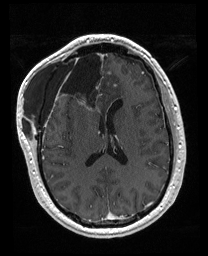
Brain MRI from a brain-tumour surgery series, one axial slice; slice 80 of 176 in the series (ordered by position); T1-weighted post-contrast; 1 mm slice thickness; 208 × 256 image matrix, field of view 208 × 256 mm. From the clinical record (not read from this slice): histopathology: Astrocytoma; WHO grade: 4; IDH mutation: yes.
Annotated regions visible in this slice (expert manual segmentation):
- previous resection cavity: bounding box <56,52,106,111> (left, top, right, bottom; pixels)